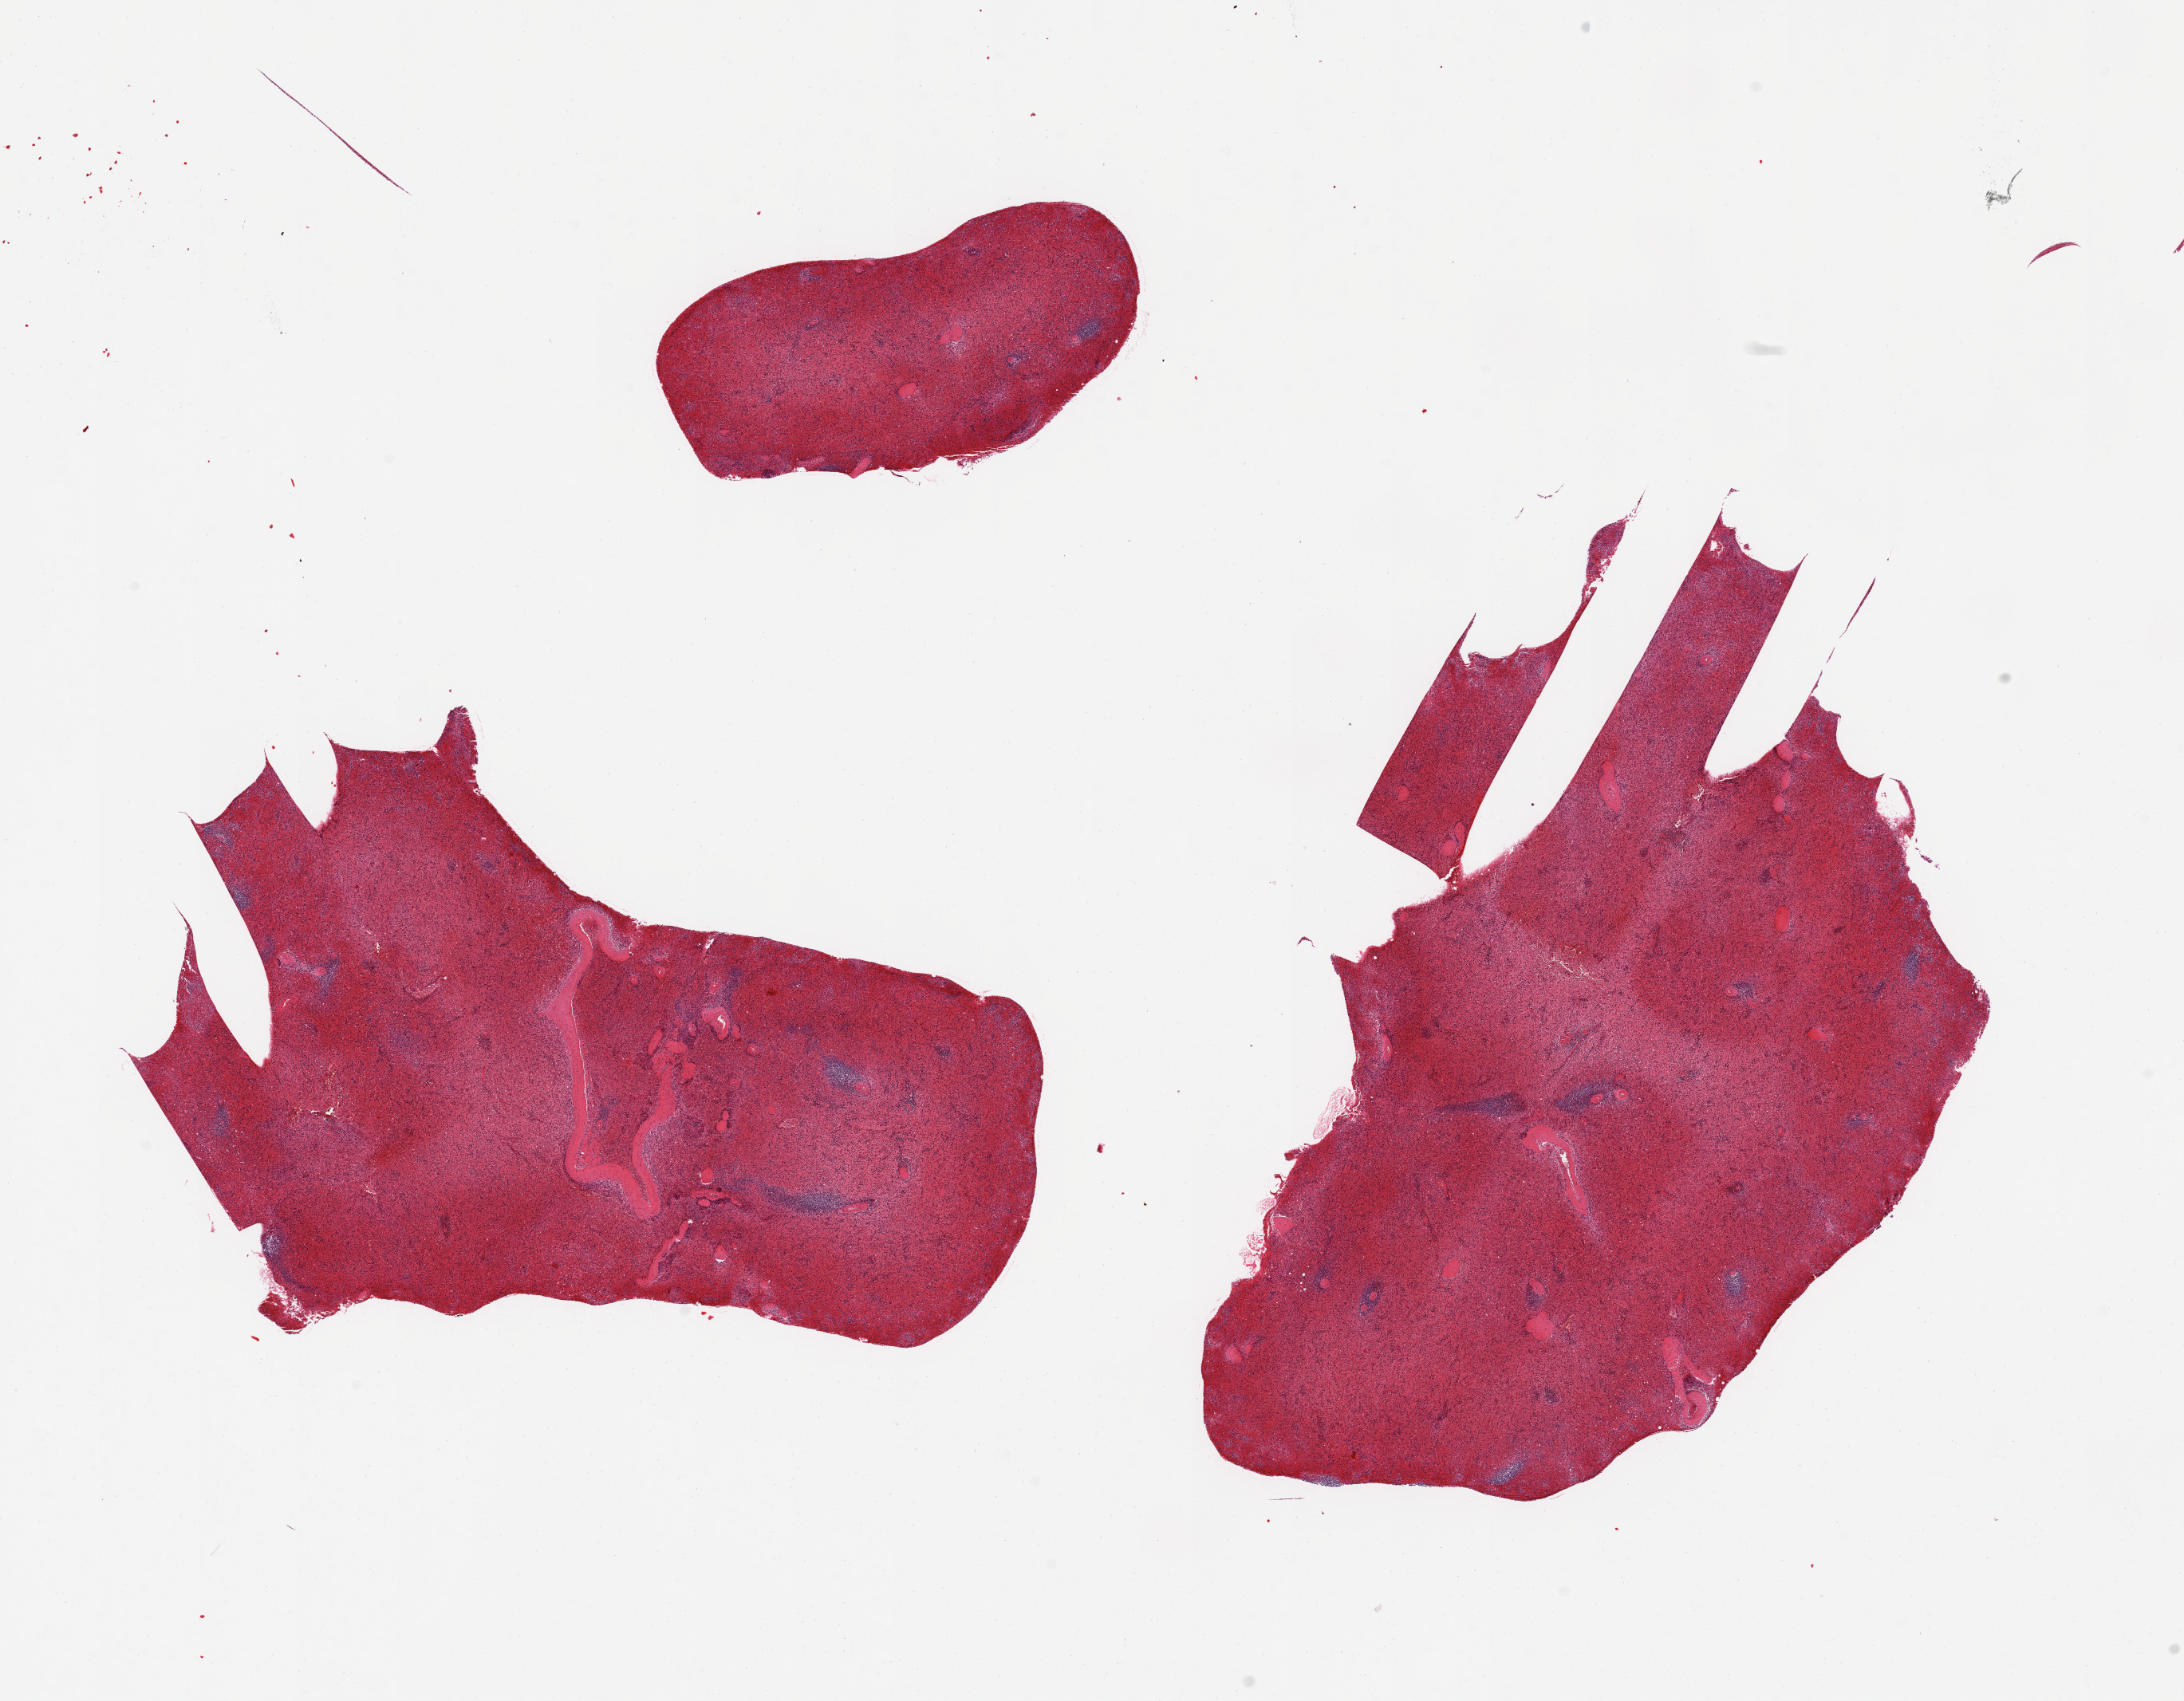
Whole-slide image, H&E stain, shown as a low-resolution overview of the whole scanned area (about 21.7 x 16.9 mm, acquisition: 20x scan), PAXgene-fixed, paraffin-embedded tissue, target tissue: spleen, donor tissue sample. Donor sex: male.
* reviewer comment on this tissue sample: 2 pieces; severe congestion